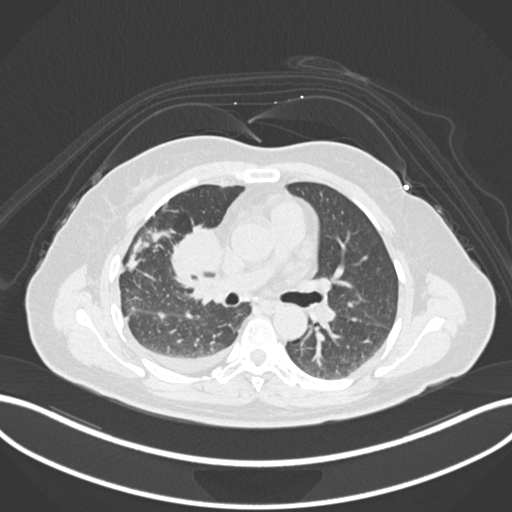
Chest CT, one axial slice; slice 80 of 172 in the series (ordered by position); reconstruction kernel B30f; 120 kVp; lung window (W 1500 / L -600 HU); 1 mm slice thickness; 512 × 512 image matrix, field of view 400 × 400 mm. Female patient, age 52 years. Case-level facts recorded for this patient, not image findings: clinical TNM (as recorded): T3 N1 M1.
Structures marked on this image (bounding box drawn by a radiologist):
- lung tumour (recorded histology: adenocarcinoma): bounding box (x1, y1, x2, y2) in pixels: (167, 220, 221, 279)